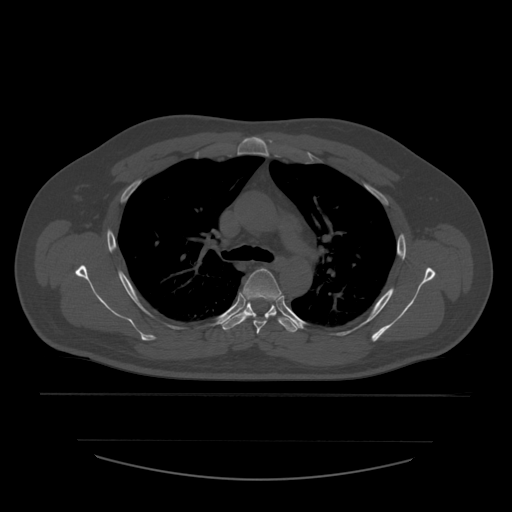
CT including the spine, one axial slice; slice 408 of 532 in the series (ordered by position); bone window (W 1800 / L 400 HU); 1.25 mm slice thickness; 512 × 512 image matrix, field of view 441 × 441 mm. Patient age 44 years. Case-level facts recorded for this patient, not image findings: primary cancer: soft tissue sarcoma.
Annotated regions visible in this slice (semi-automatically segmented with operator editing):
- T4 vertebra: bounding box [x1, y1, x2, y2] px = [243, 268, 282, 334]
- T5 vertebra: [222, 303, 298, 333]